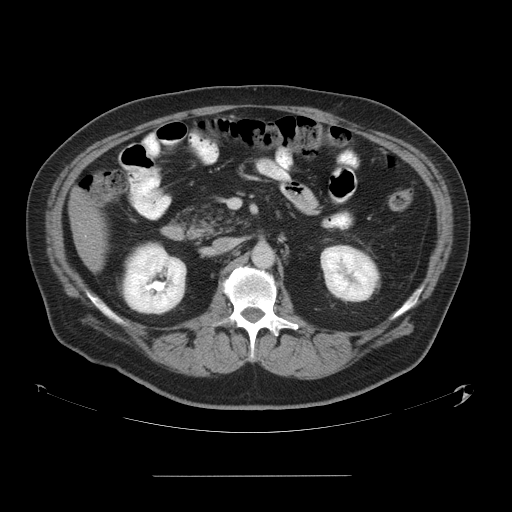
Contrast-enhanced abdominal CT, one axial slice. Position 22 of 58 along the scan axis. Intravenous contrast given. Soft-tissue window (W 400 / L 40 HU). 512 × 512 image matrix, field of view 480 × 480 mm. Male patient, age 63 years. From the clinical record (not read from this slice): diagnosis: colorectal cancer liver metastases, imaged before liver resection; multiple liver metastases: no; largest metastasis: 4.2 cm; chemotherapy before resection: yes.
Annotated regions visible in this slice (outlined manually by an expert reader):
- liver: box from (x=71, y=191) to (x=104, y=269) px
- planned liver remnant (the part of the liver to remain after resection): (x=71, y=191)–(x=104, y=269)